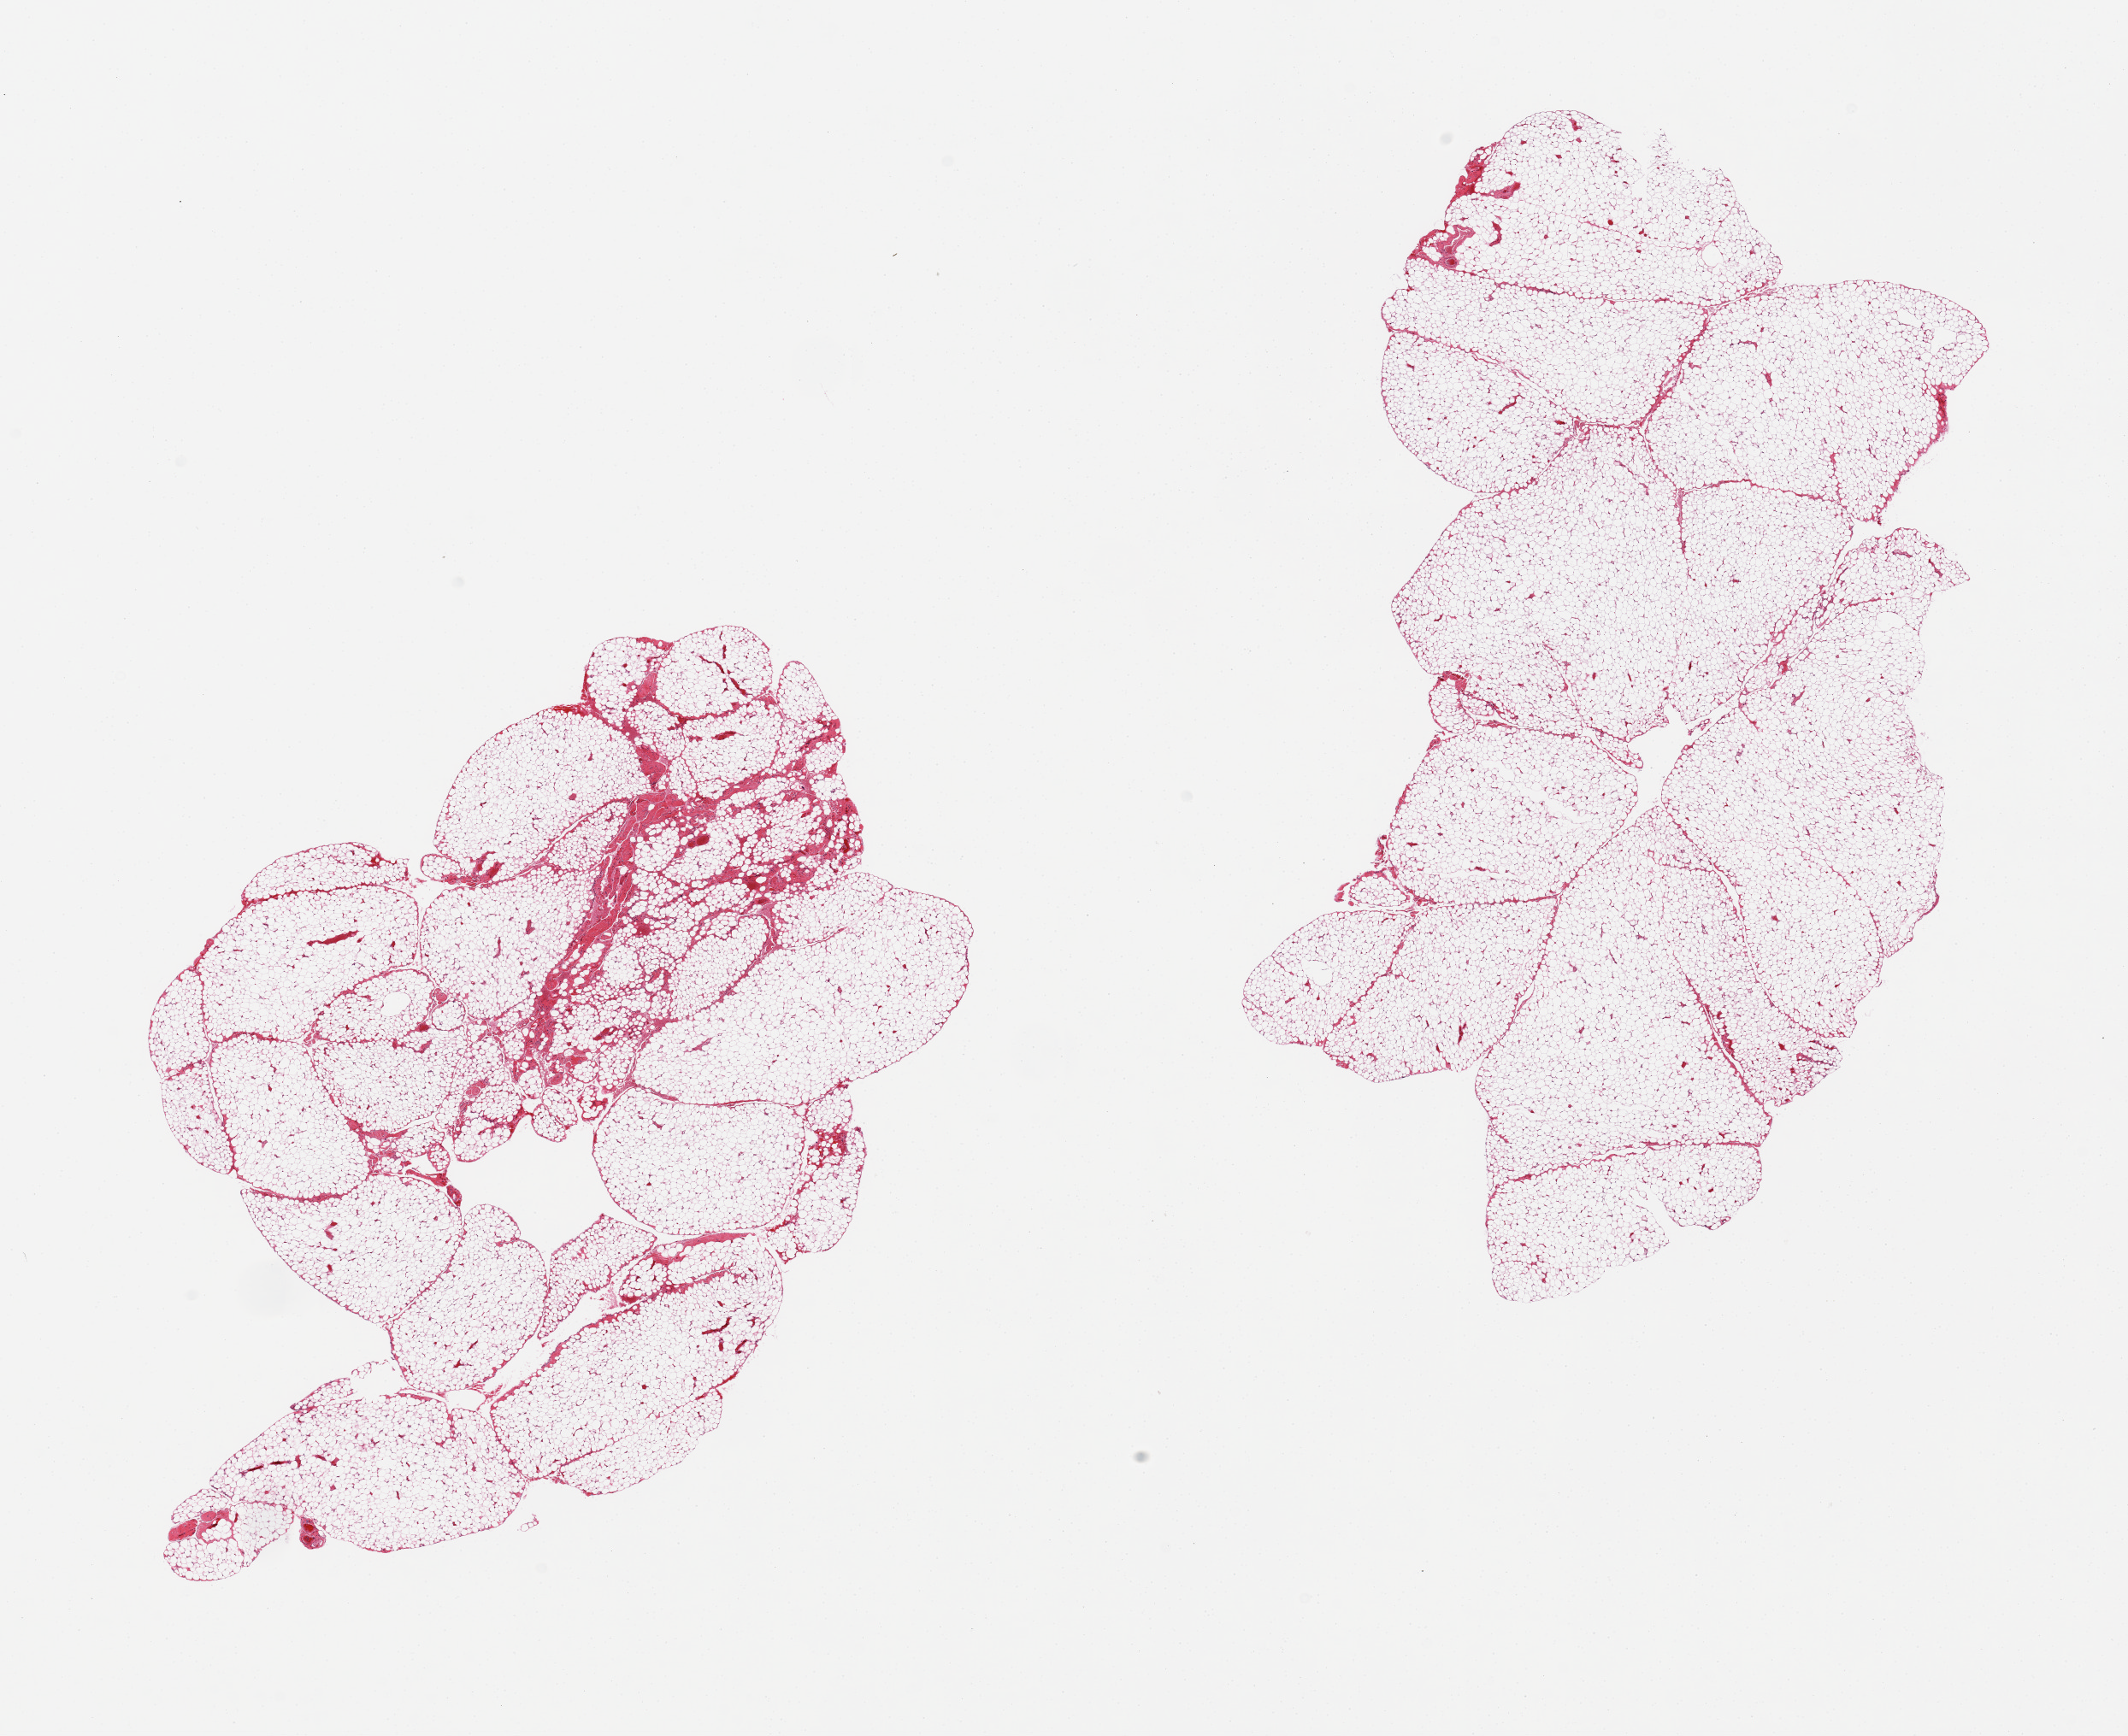
Digitized hematoxylin and eosin (H&E)-stained section, brightfield — a low-resolution overview of the entire scanned area, about 19.7 x 16.1 mm (acquisition: 20x scan). PAXgene-fixed, paraffin-embedded tissue. Section of omentum (target tissue). Donor tissue sample. Donor: male.
Pathologist's review note for this sample: 2 pieces, ~10% fibrous/mesothelial hyperplastic tissue.